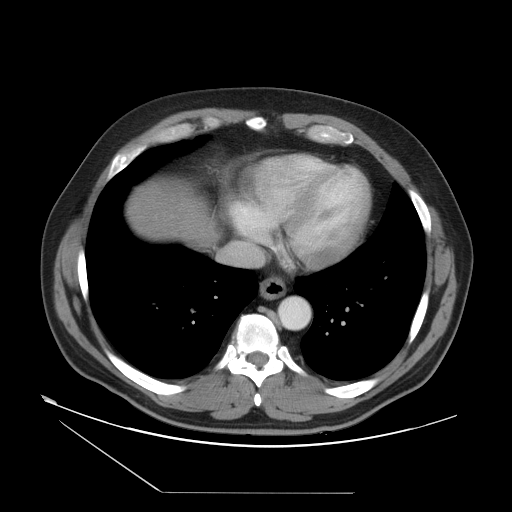
Contrast-enhanced abdominal CT, one axial slice; position 49 of 55 along the scan axis; reconstruction kernel STANDARD; 120 kVp; soft-tissue window (W 400 / L 40 HU); 512 × 512 image matrix. Male patient, age 59 years. From the clinical record (not read from this slice): diagnosis: colorectal cancer liver metastases, imaged before liver resection; multiple liver metastases: yes; largest metastasis: 0.3 cm.
Outlined on this slice (outlined manually by an expert reader):
- hepatic veins: bounding box <225,233,267,264> (left, top, right, bottom; pixels)
- liver: <131,186,215,240>
- planned liver remnant (the part of the liver to remain after resection): <131,188,178,234>